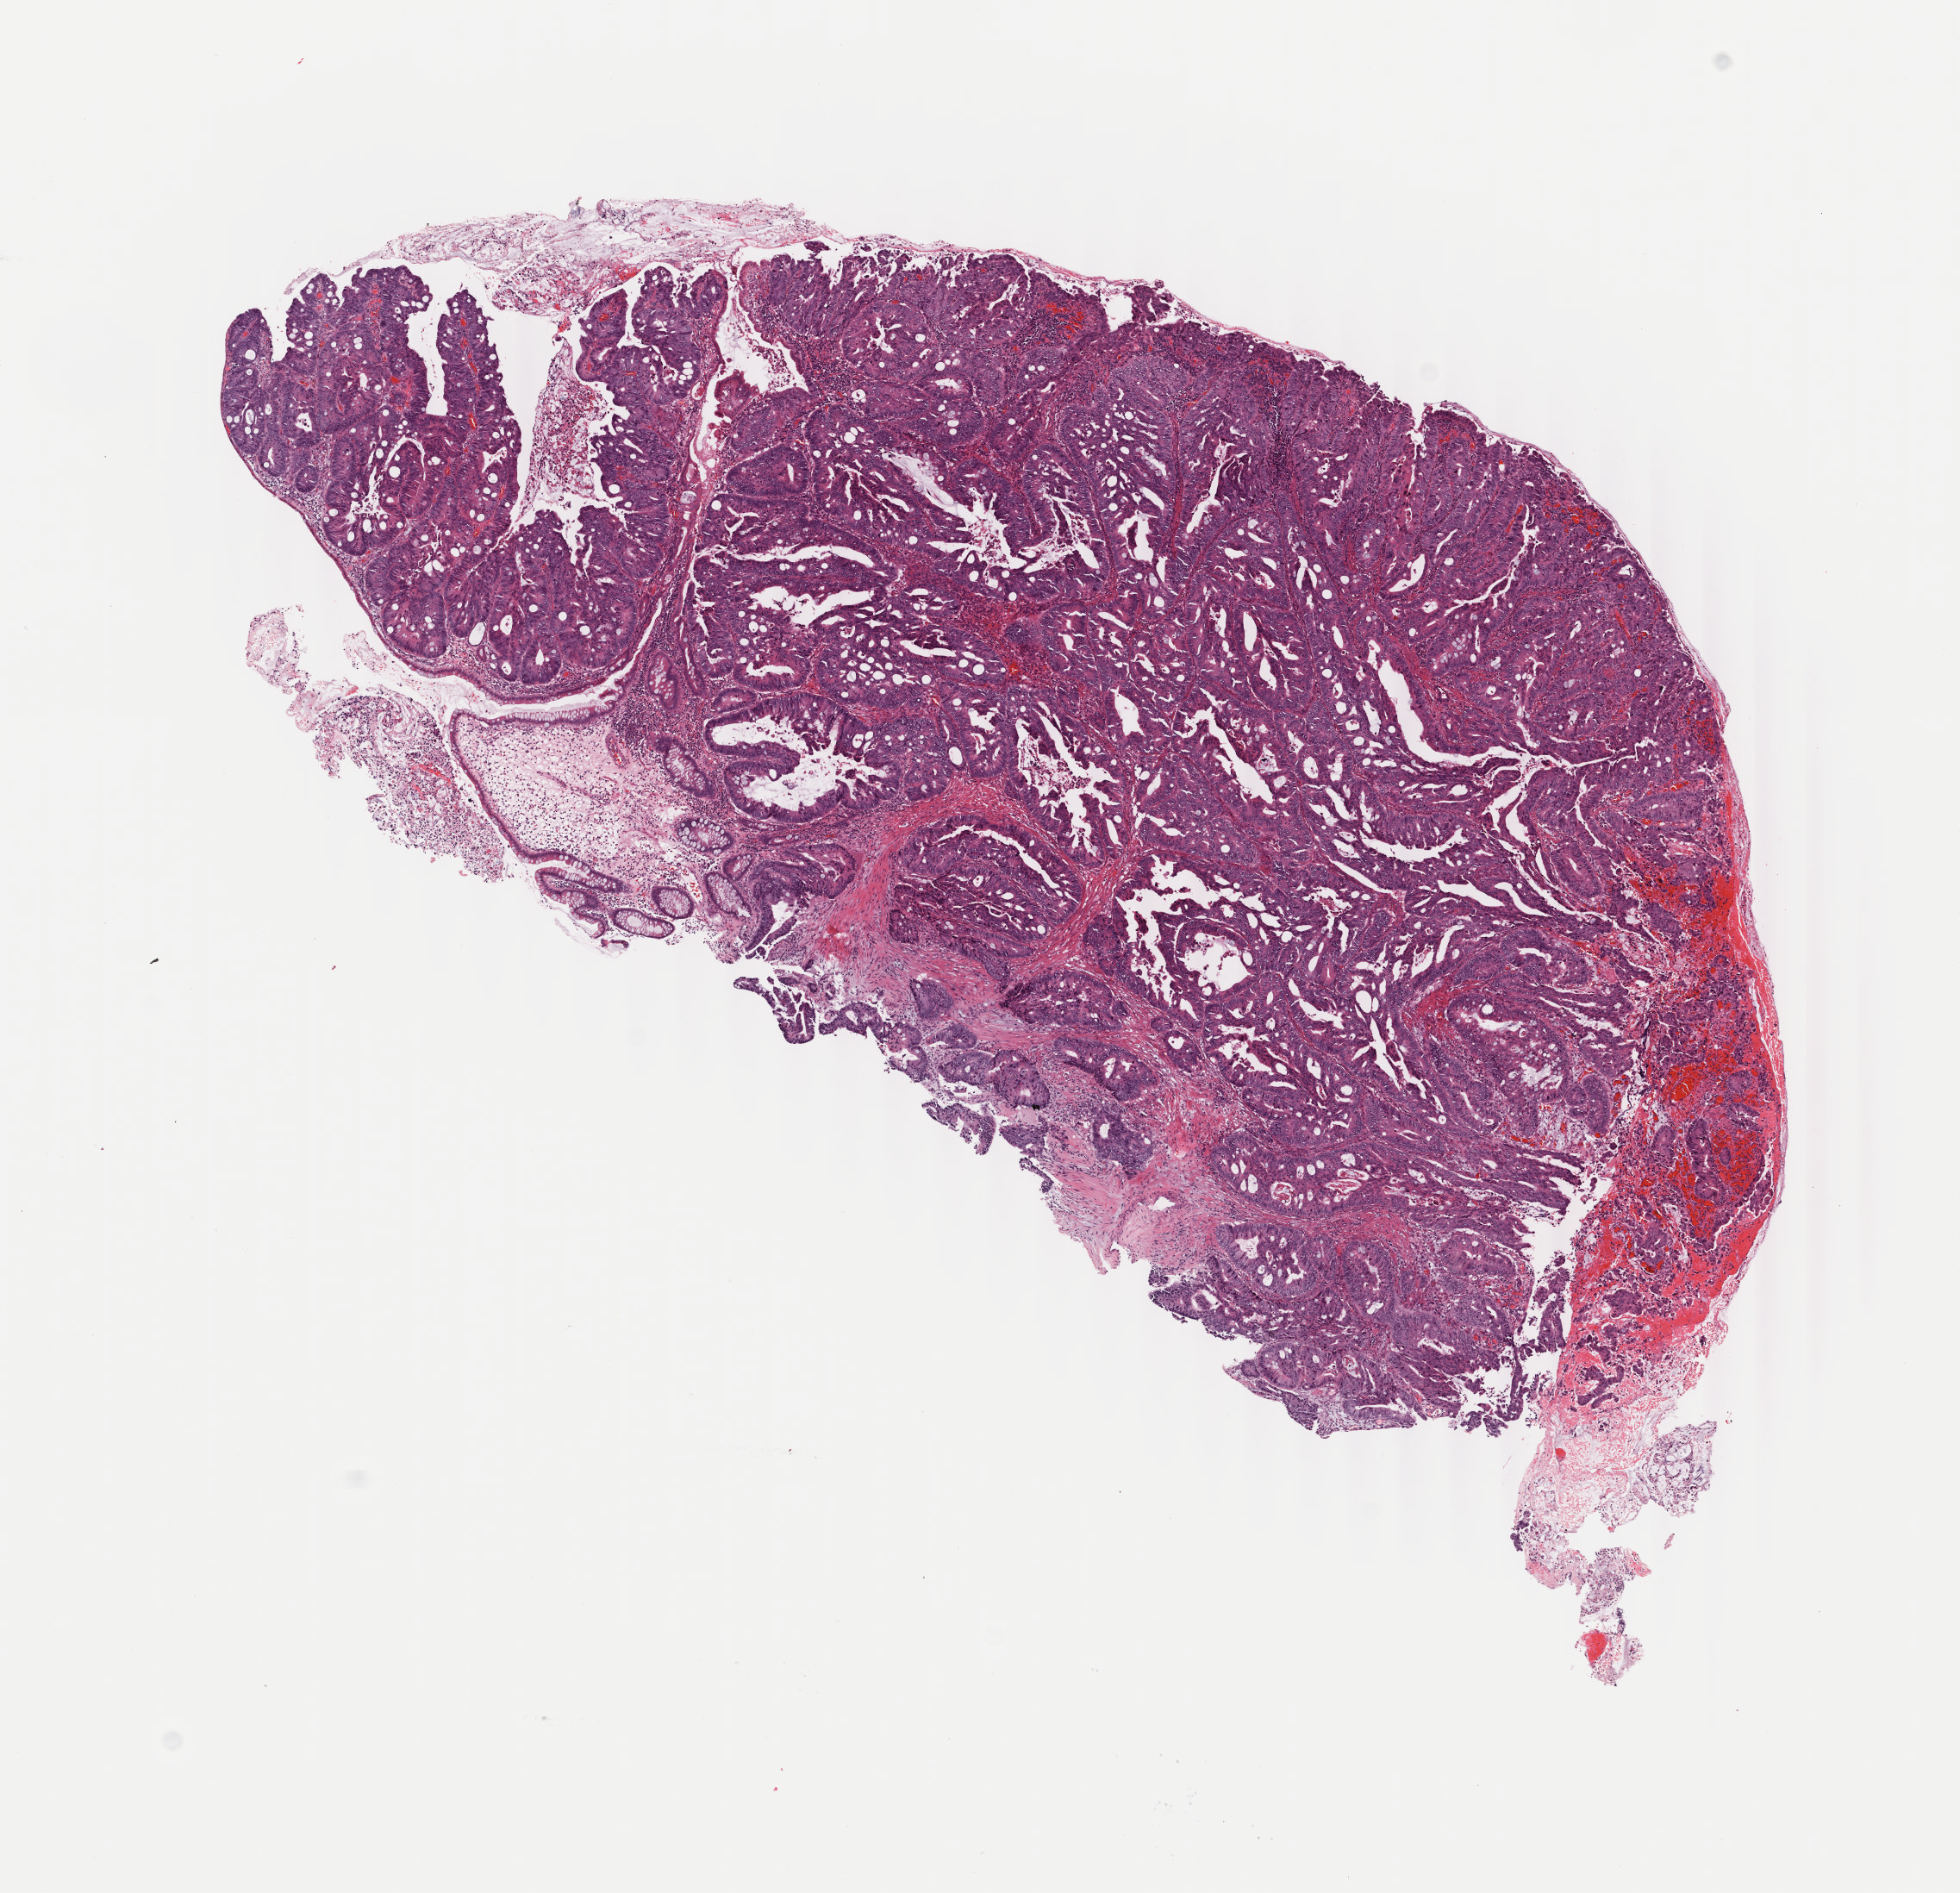
H&E-stained whole-slide image — a low-resolution overview of the entire scanned area, about 9.0 x 8.7 mm (slide scanned at 40x); frozen section; primary tumour sample from the colon. Female, age 69 years at initial diagnosis. Slide review estimates, as recorded: tumour cells 97%, tumour nuclei 92%, normal cells 3%, stromal cells 0%, necrosis 0%. Inflammatory infiltration, as recorded: lymphocyte infiltration 0%, monocyte infiltration 0%, neutrophil infiltration 0%.
* diagnosis: Adenocarcinoma, NOS (ascending colon)
* AJCC pathologic stage: IIA (7th edition)
* TNM: T3 N0 M0